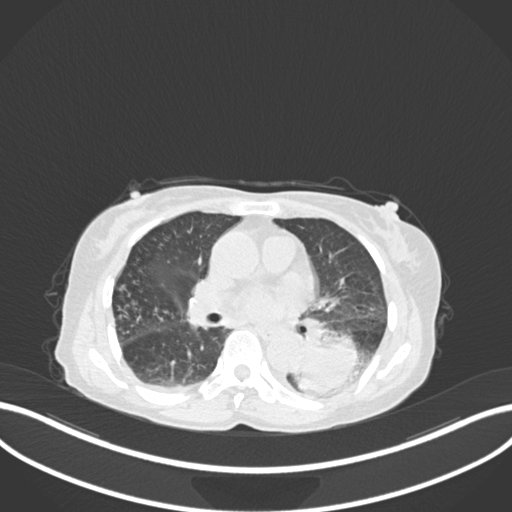
Chest CT, one axial slice; slice 87 of 233 in the series (ordered by position); reconstruction kernel B30f; lung window (W 1500 / L -600 HU); 1 mm slice thickness; 512 × 512 image matrix, field of view 400 × 400 mm. Female patient, age 78 years. From the clinical record (not read from this slice): clinical TNM (as recorded): T3 N0 M1.
Outlined on this slice (bounding box drawn by a radiologist):
- lung tumour (recorded histology: squamous cell carcinoma): bounding box <296,328,362,393> (left, top, right, bottom; pixels)